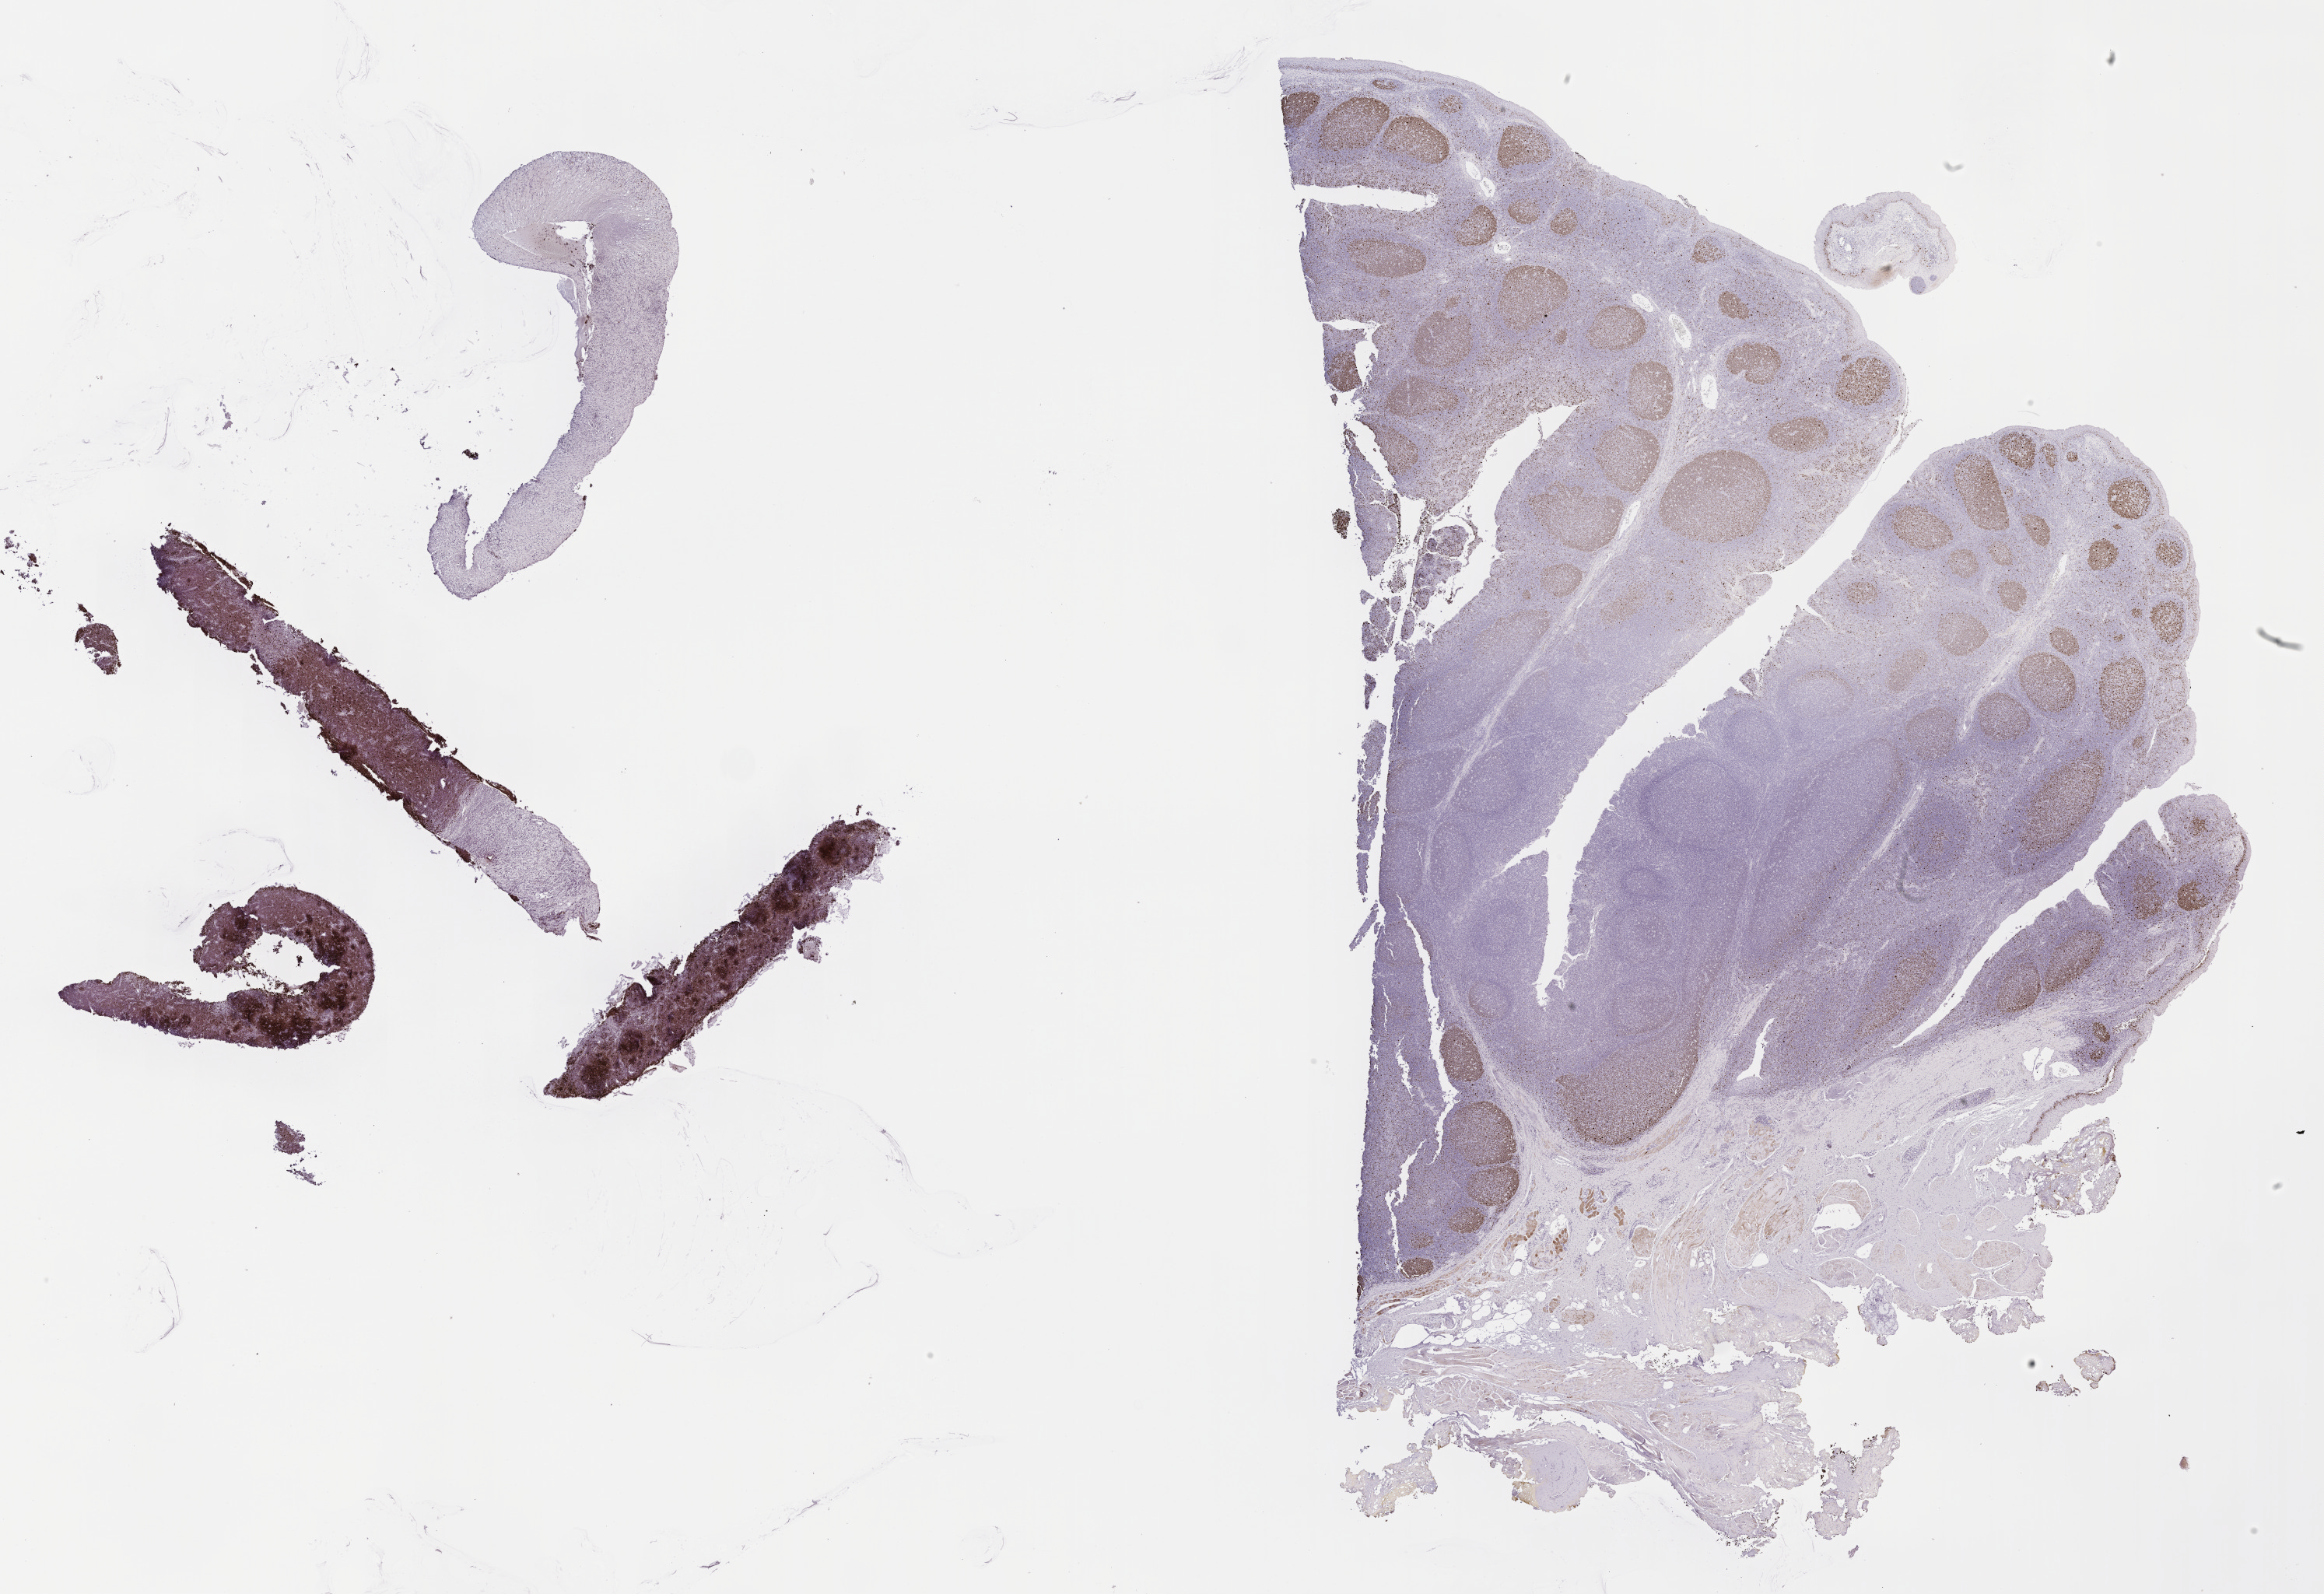
IHC for Ki-67, whole-slide image, low-resolution overview of the scanned area, about 24.2 x 16.6 mm. Patient sex: male.
Specimen: tumor tissue.